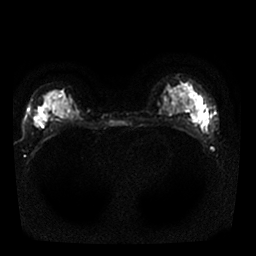
Breast MRI, one axial slice; slice 14 of 25 in the series (ordered by position); diffusion-weighted series; image 2 of 4 stored at this slice position (different b-values; order by instance number); 1.5 T; 256 × 256 image matrix. Female patient.
Outlined on this slice (outlined manually by an expert reader):
- tumour on diffusion-weighted imaging: bounding box <192,112,206,125> (left, top, right, bottom; pixels)